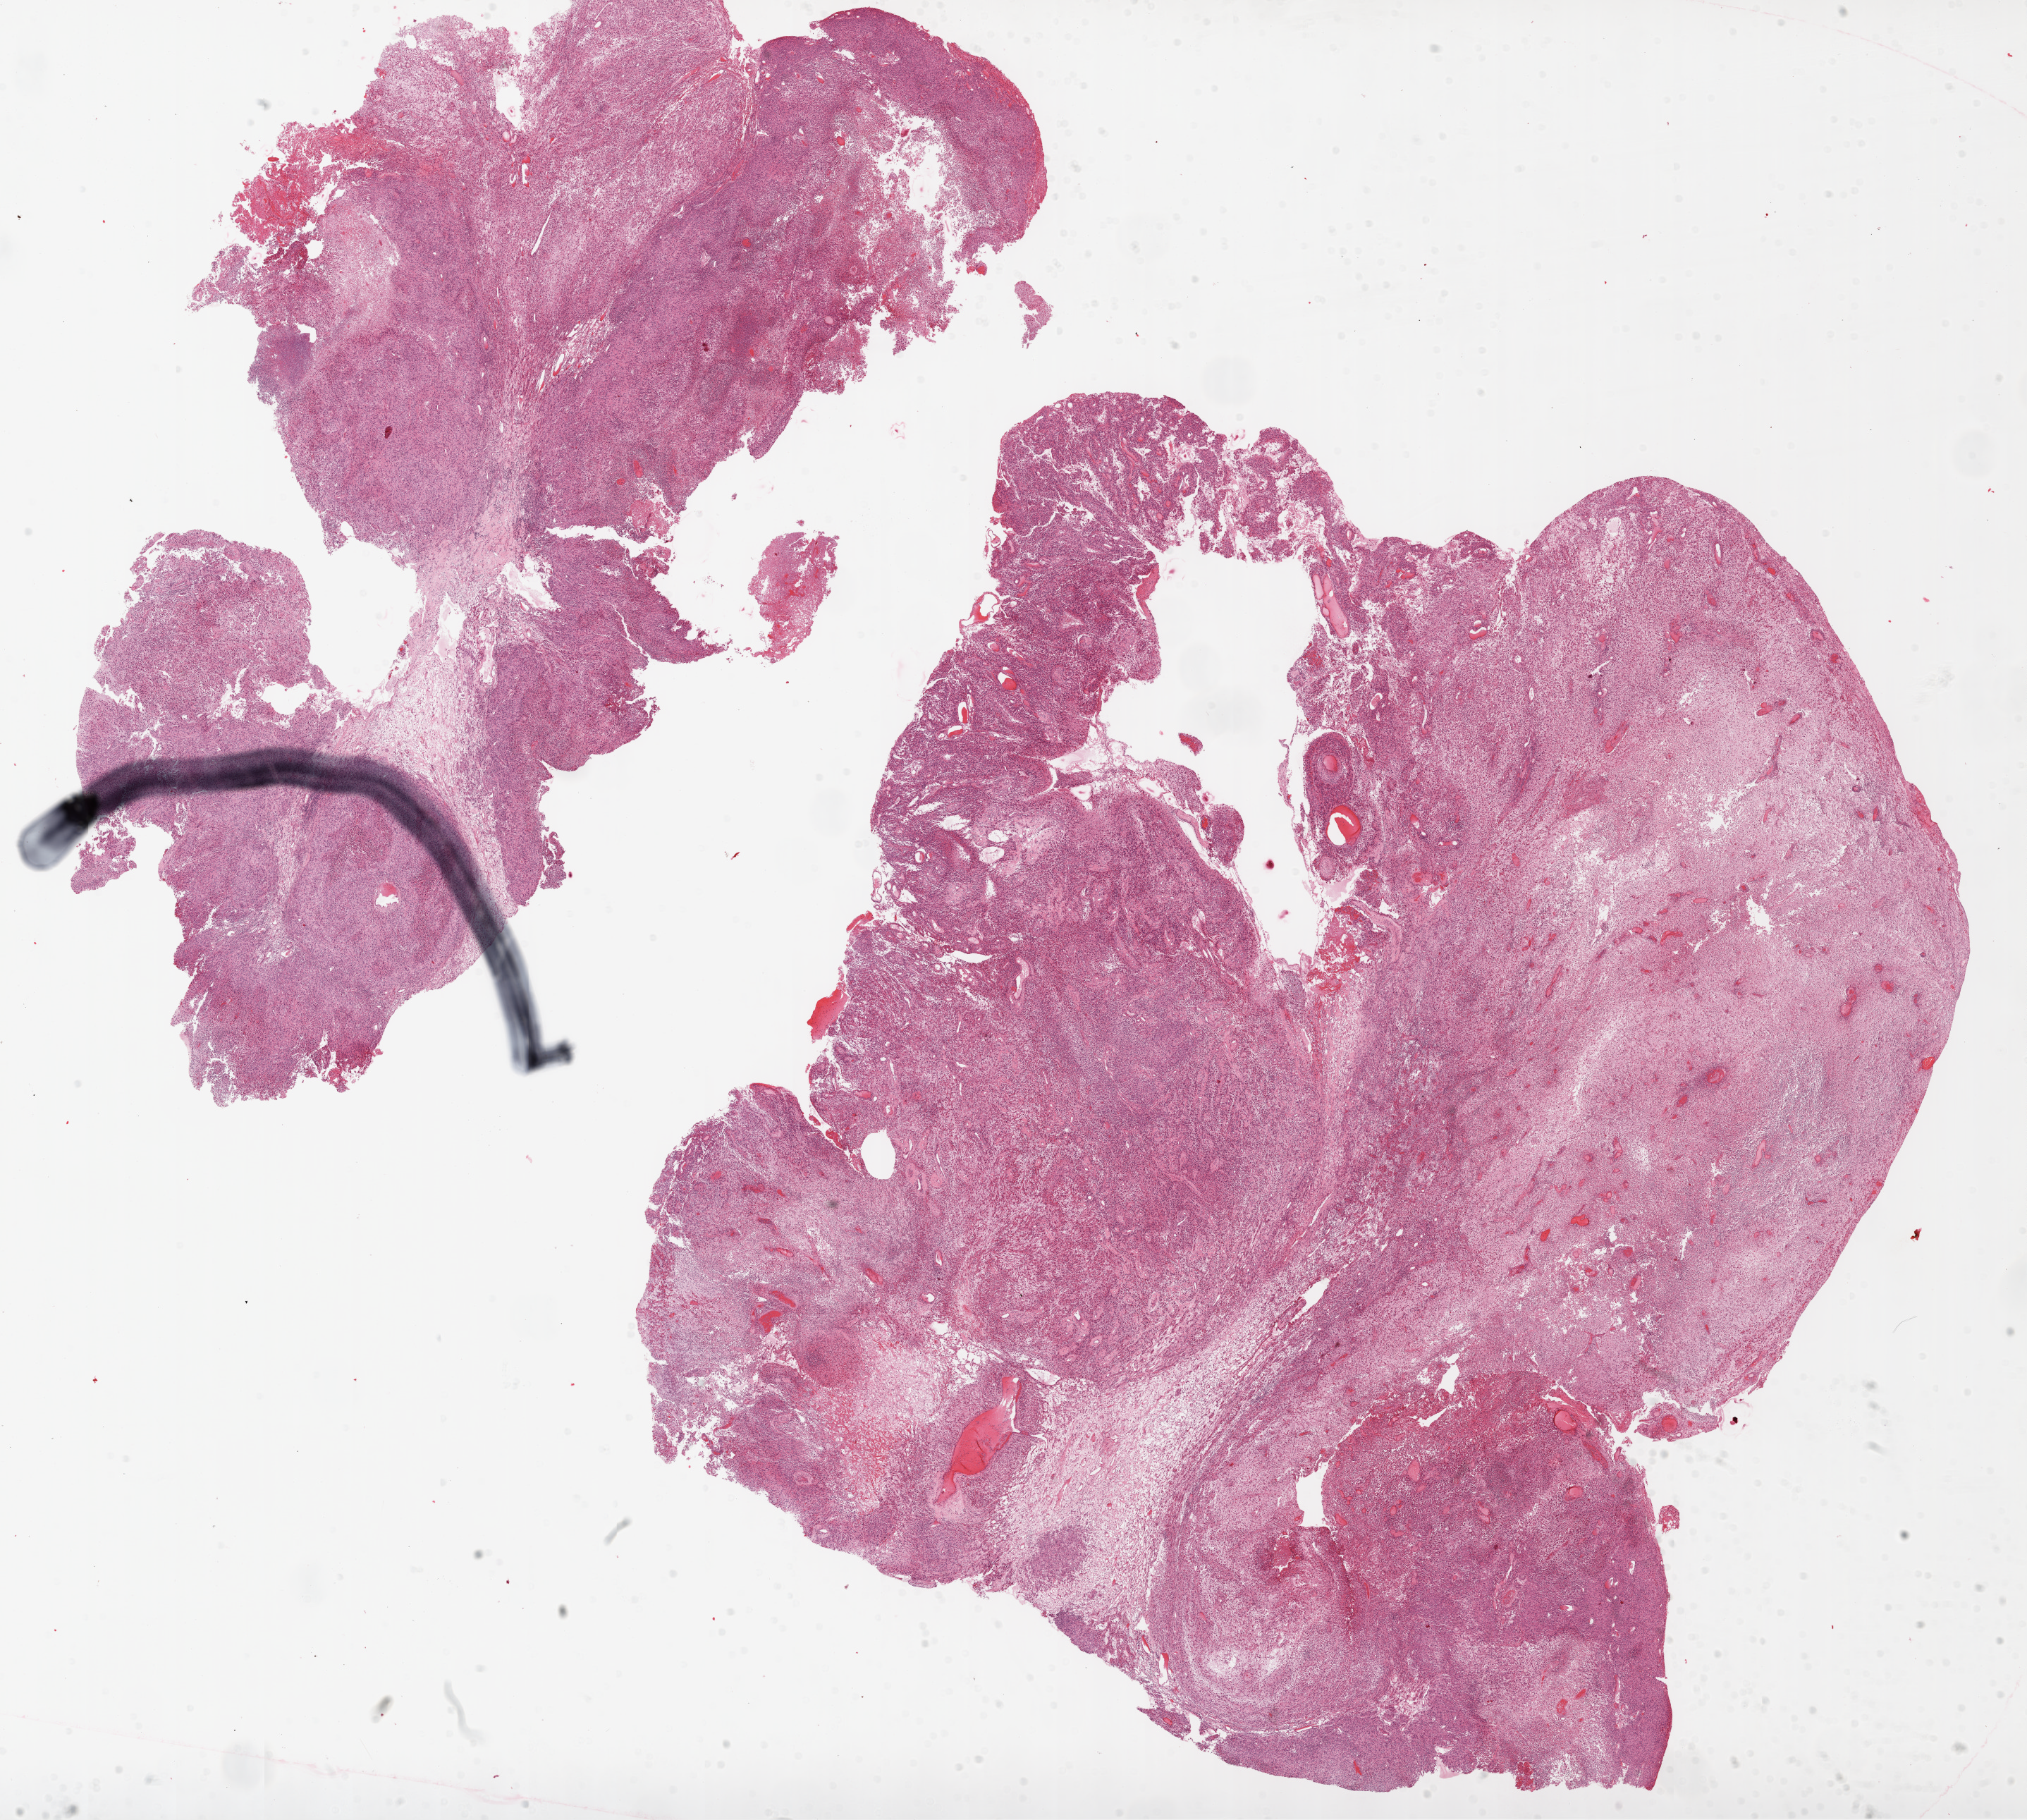
Digitized Hematoxylin and eosin (H&E) stained tissue section (whole slide) — whole scanned area (about 23.1 x 20.7 mm) shown as a low-resolution overview. Formalin-fixed paraffin-embedded (FFPE) diagnostic section. Sample: primary tumour, brain. Female patient; age at initial diagnosis 59 years.
* diagnosis: Glioblastoma